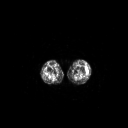
FDG PET of an extremity soft-tissue mass (from a PET/CT study), one axial slice; position 165 of 223 along the scan axis; 3.27 mm slice thickness; 128 × 128 image matrix, field of view 700 × 700 mm. Female patient, age 16 years. Case-level facts recorded for this patient, not image findings: histological type: spindle cell suggestive of biphasic synovial sarcoma; grade: intermediate; site of the primary tumour: left knee.
Outlined on this slice (expert contour drawn on MRI and transferred to this co-registered scan by the dataset authors):
- gross tumour volume including surrounding oedema: box from (x=85, y=67) to (x=88, y=72) px
- gross tumour volume (mass): (x=85, y=67)–(x=88, y=72)